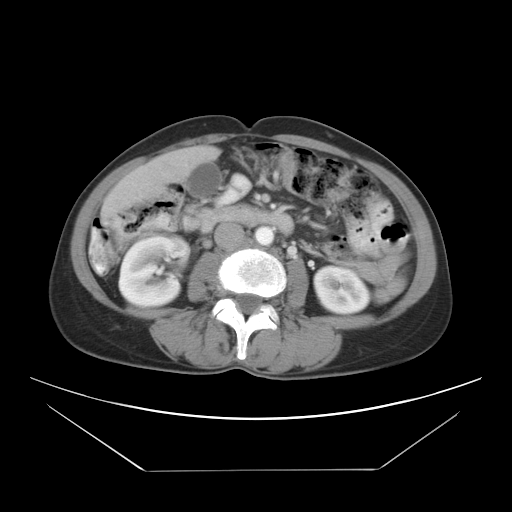
Contrast-enhanced abdominal CT, one axial slice. Slice 7 of 30 in the series (ordered by position). Reconstruction kernel STANDARD. 120 kVp. Intravenous contrast given. Soft-tissue window (W 400 / L 40 HU). 7.5 mm slice thickness. 512 × 512 image matrix, field of view 412 × 412 mm. Female patient, age 54 years. From the clinical record (not read from this slice): diagnosis: colorectal cancer liver metastases, imaged before liver resection; multiple liver metastases: yes.
Structures marked on this image (expert manual segmentation):
- liver: bounding box [x1, y1, x2, y2] px = [106, 148, 211, 213]
- planned liver remnant (the part of the liver to remain after resection): [119, 148, 211, 192]